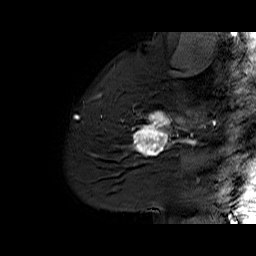
Breast MRI (dynamic contrast-enhanced), one sagittal slice. Slice 47 of 60 in the series (ordered by position). Dynamic contrast-enhanced series, time point 2 of 6 at this slice position (early post-contrast). 1.5 T. TE 6.1 ms, TR 32.9 ms. 4 mm slice thickness. 256 × 256 image matrix, field of view 220 × 220 mm. Female patient. Case-level facts recorded for this patient, not image findings: setting: breast cancer imaged before/during neoadjuvant chemotherapy; receptor status: HER2-positive.
Structures marked on this image (semi-automatically segmented with operator editing):
- analysis volume of interest (the breast-tissue region the enhancement analysis was run in; not a lesion): bounding box [x1, y1, x2, y2] px = [127, 95, 194, 165]
- tumour enhancement mask (voxels above the 100 % enhancement threshold inside the analysis volume of interest): [131, 111, 193, 155]